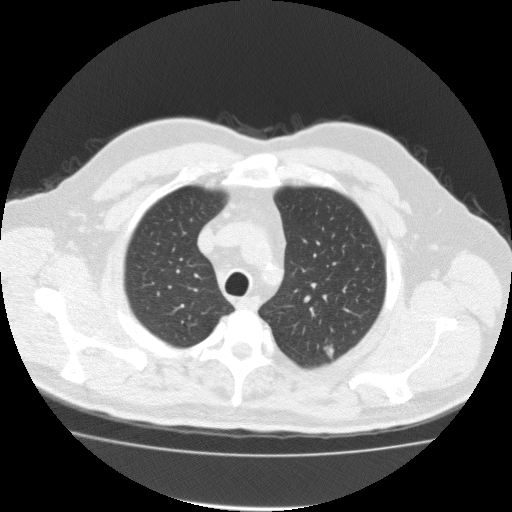
Chest CT (low-dose screening protocol), one axial image; first (baseline) screen; lung window (W 1500 / L -600 HU); 2 mm slice thickness. Male, age 57 years at enrolment. Former smoker at enrolment.
Expert-annotated lung lesion, bounding box <318,336,348,368> (left, top, right, bottom; pixels). Screening reader's record for this exam (one nodule recorded; not confirmed to be the boxed lesion): non-calcified nodule or mass ≥4 mm, left upper lobe, 11 × 8 mm, spiculated (stellate) margins, soft tissue attenuation. Official screen result: positive, change unspecified: nodule(s) >= 4 mm or enlarging nodule(s), mass(es), or other non-specific abnormalities suspicious for lung cancer. Later outcome: lung cancer diagnosed 19 days after this screen — bronchiolo-alveolar adenocarcinoma, NOS, left upper lobe, well differentiated (G1), stage IA (AJCC 6th edition), 80 mm at pathology.